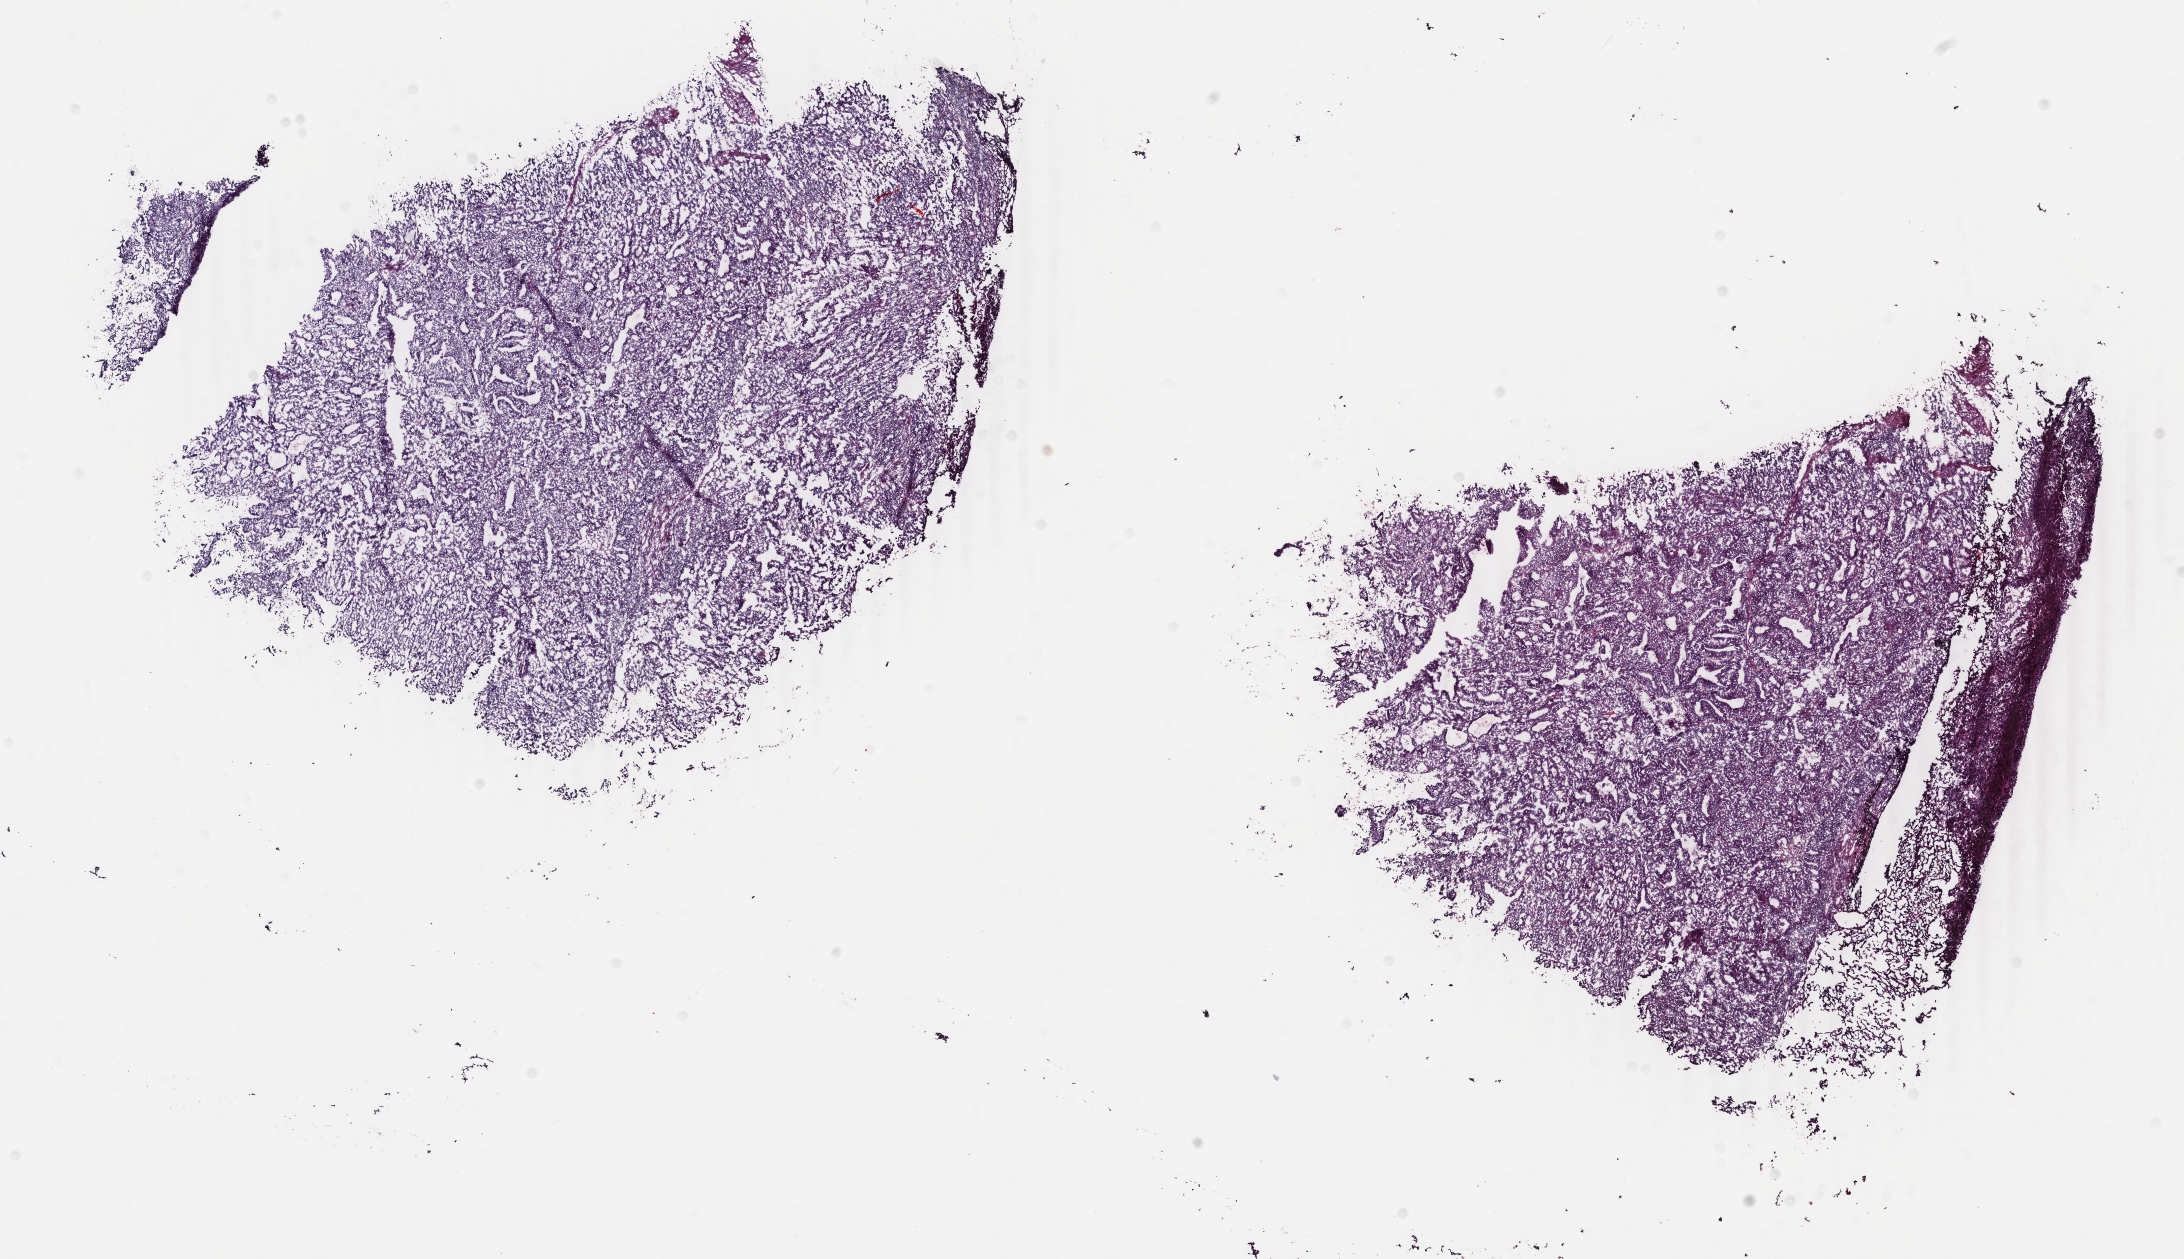
Hematoxylin and eosin (H&E) stained whole-slide image, shown as a low-resolution overview of the whole scanned area (about 17.4 x 10.0 mm). Frozen section from the bottom of the tissue portion. Sample: primary tumour, uterus. Patient: female, age at initial diagnosis 58 years.
Pathologic diagnosis: Endometrioid adenocarcinoma, NOS (endometrium).